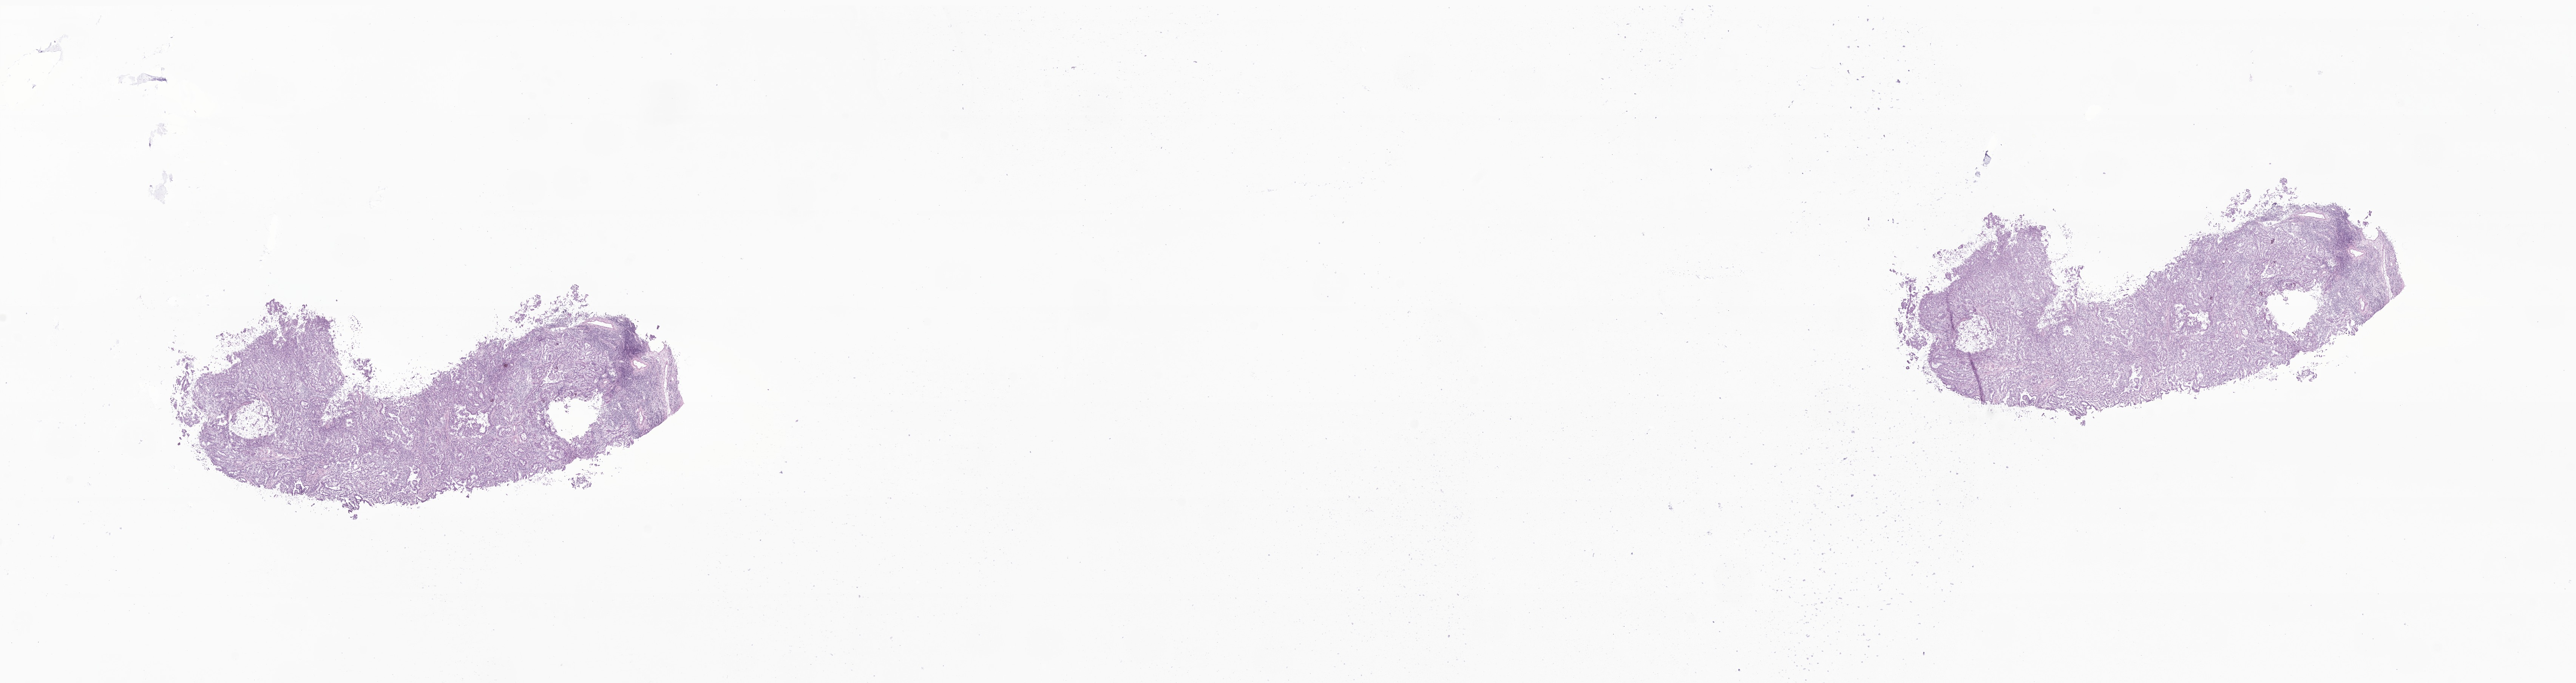
Whole-slide image, H&E stain of tumor tissue from the thyroid — low-resolution overview of the scanned area, about 28.8 x 7.6 mm; cryosection (OCT / tissue freezing medium). Patient: female, age 175 months (14 years 7 months).
Recorded diagnosis: Papillary carcinoma, NOS.